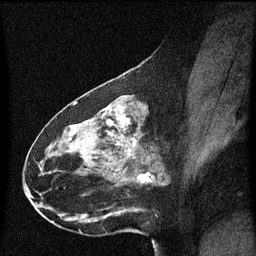
Breast MRI (dynamic contrast-enhanced), one sagittal slice. Position 29 of 60 along the scan axis. Dynamic contrast-enhanced series, image 2 of 3 at this slice position (ordered by acquisition). 1.5 T. TE 4.2 ms, TR 8.4 ms. 2 mm slice thickness. 256 × 256 image matrix, field of view 200 × 200 mm. Patient: female, 49 years. From the clinical record (not read from this slice): setting: breast cancer imaged before/during neoadjuvant chemotherapy; receptor status: HR-positive, HER2-negative.
Structures marked on this image (semi-automatically segmented with operator editing):
- analysis volume of interest (the breast-tissue region the enhancement analysis was run in; not a lesion): bounding box (x1, y1, x2, y2) in pixels: (27, 96, 171, 221)
- tumour enhancement mask (voxels above the 70 % enhancement threshold inside the analysis volume of interest): (105, 114, 137, 147)